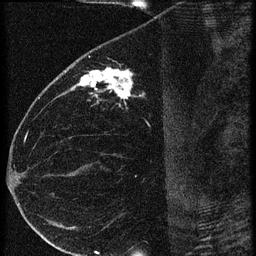
Breast MRI (dynamic contrast-enhanced), one sagittal slice. 3 images stored at this slice position (order not interpretable as contrast timing). 1.5 T. TE 4.2 ms, TR 20.4 ms. 1.5 mm slice thickness. 256 × 256 image matrix, field of view 180 × 180 mm. Female patient, age 35 years. From the clinical record (not read from this slice): setting: breast cancer imaged before/during neoadjuvant chemotherapy; receptor status: HR-positive, HER2-negative.
Structures marked on this image (semi-automatically segmented with operator editing):
- analysis volume of interest (the breast-tissue region the enhancement analysis was run in; not a lesion): bounding box (x1, y1, x2, y2) in pixels: (65, 60, 169, 119)
- tumour enhancement mask (voxels above the 90 % enhancement threshold inside the analysis volume of interest): (71, 68, 131, 99)